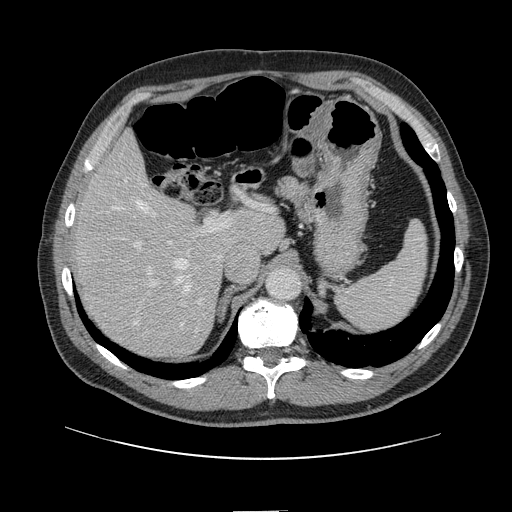
Contrast-enhanced abdominal CT, one axial slice; slice 93 of 161 in the series (ordered by position); 120 kVp; soft-tissue window (W 400 / L 40 HU); 512 × 512 image matrix, field of view 412 × 412 mm. Male patient, age 66 years. From the clinical record (not read from this slice): diagnosis: colorectal cancer liver metastases, imaged before liver resection; multiple liver metastases: no; largest metastasis: 3.5 cm; disease in both lobes: no.
Annotated regions visible in this slice (outlined manually by an expert reader):
- hepatic veins: bounding box (x1, y1, x2, y2) in pixels: (107, 178, 190, 324)
- liver: (77, 137, 282, 357)
- planned liver remnant (the part of the liver to remain after resection): (77, 136, 282, 305)
- portal vein (with intrahepatic branches): (118, 217, 230, 306)